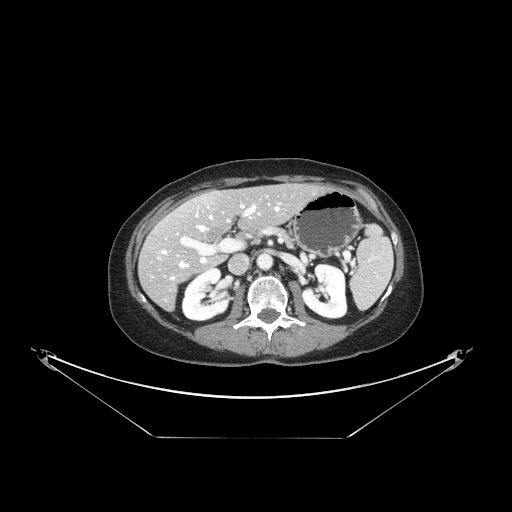
Contrast-enhanced abdominal CT, one axial slice; slice 78 of 148 in the series (ordered by position); intravenous contrast given; soft-tissue window (W 400 / L 40 HU); 2.5 mm slice thickness; 512 × 512 image matrix, field of view 500 × 500 mm. Female patient, age 73 years. From the clinical record (not read from this slice): diagnosis: colorectal cancer liver metastases, imaged before liver resection; multiple liver metastases: no; largest metastasis: 1 cm; disease in both lobes: no.
Outlined on this slice (expert manual segmentation):
- hepatic veins: bounding box [x1, y1, x2, y2] px = [159, 203, 280, 280]
- liver: [140, 184, 322, 309]
- planned liver remnant (the part of the liver to remain after resection): [168, 184, 322, 240]
- portal vein (with intrahepatic branches): [177, 204, 260, 264]